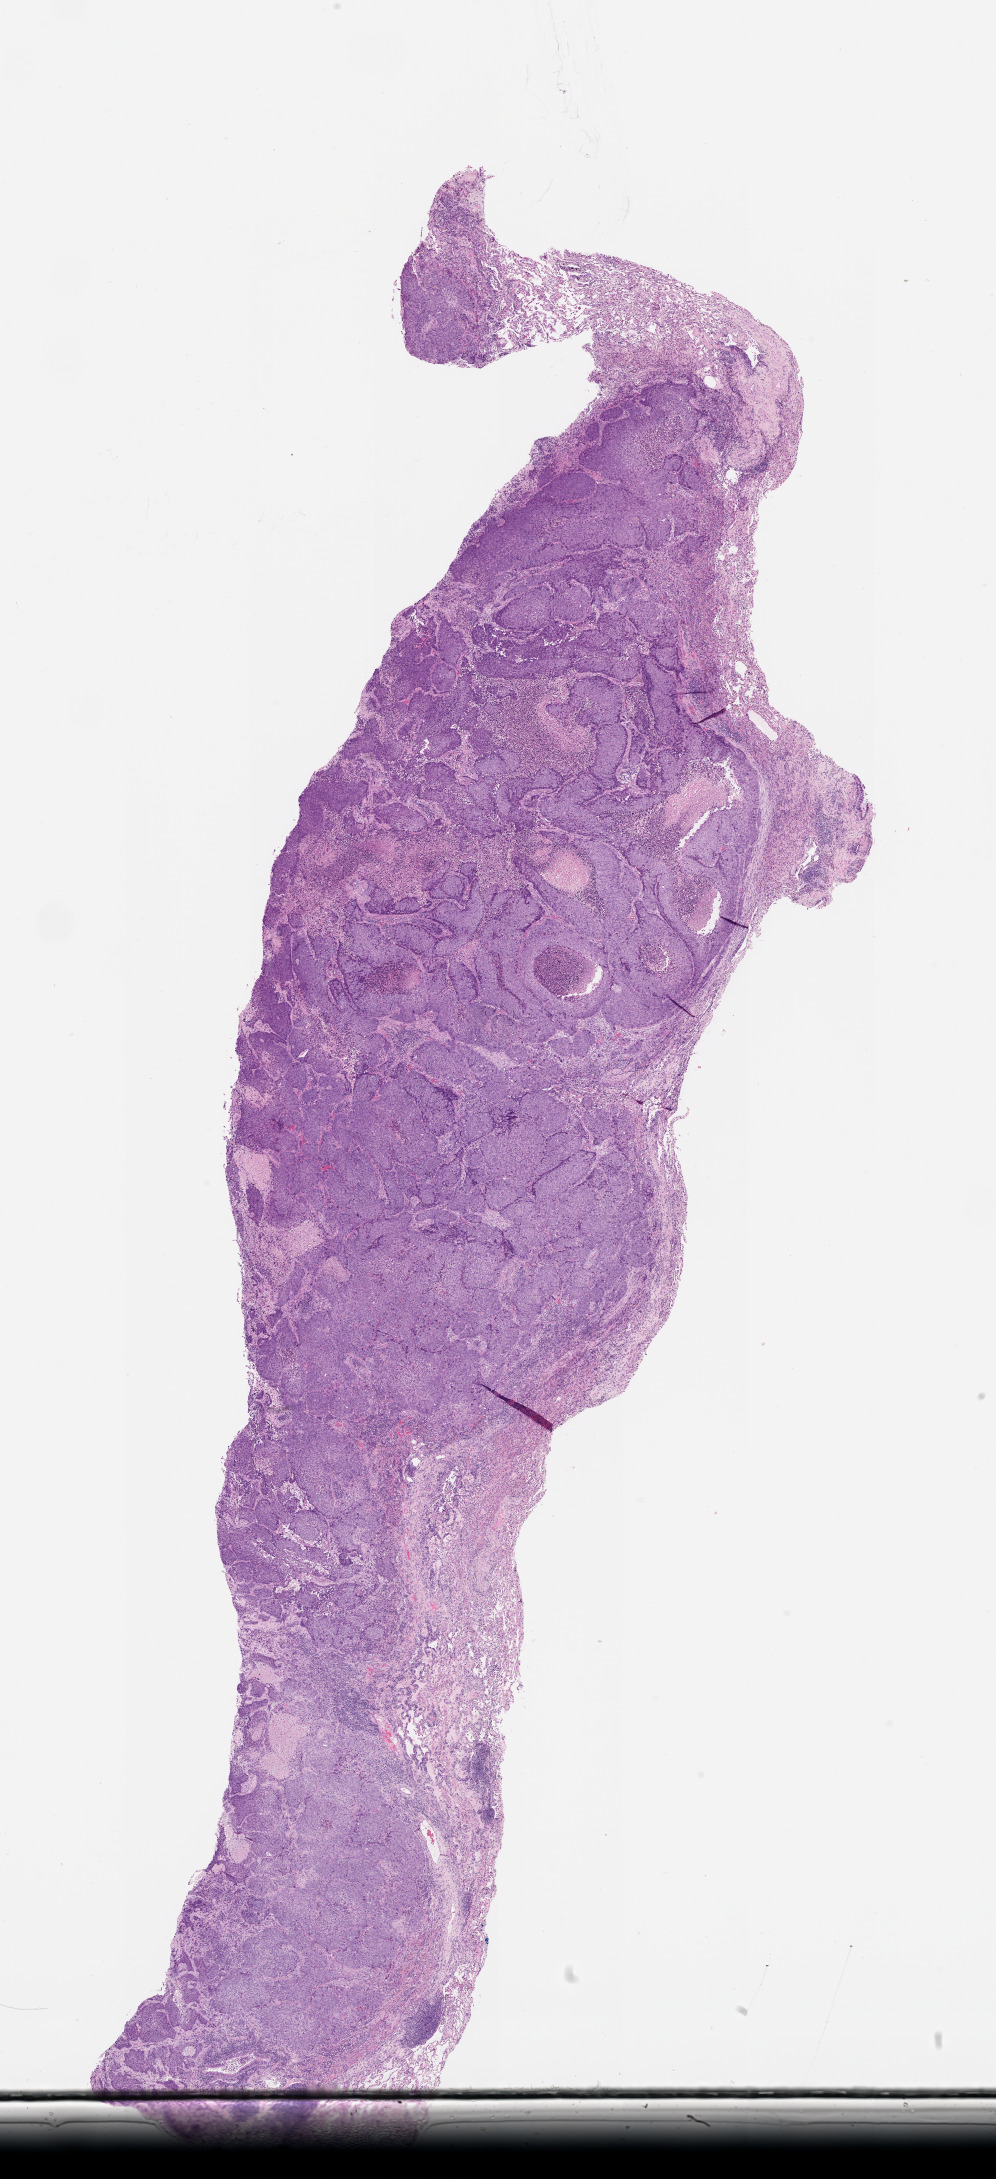
Whole-slide histology image, H&E — shown as a low-resolution overview of the whole scanned area (about 8.0 x 17.5 mm); tumour tissue sample, lung. Patient: male, age 56 years.
Patient diagnosis (cohort enrolment): squamous cell carcinoma (lung).